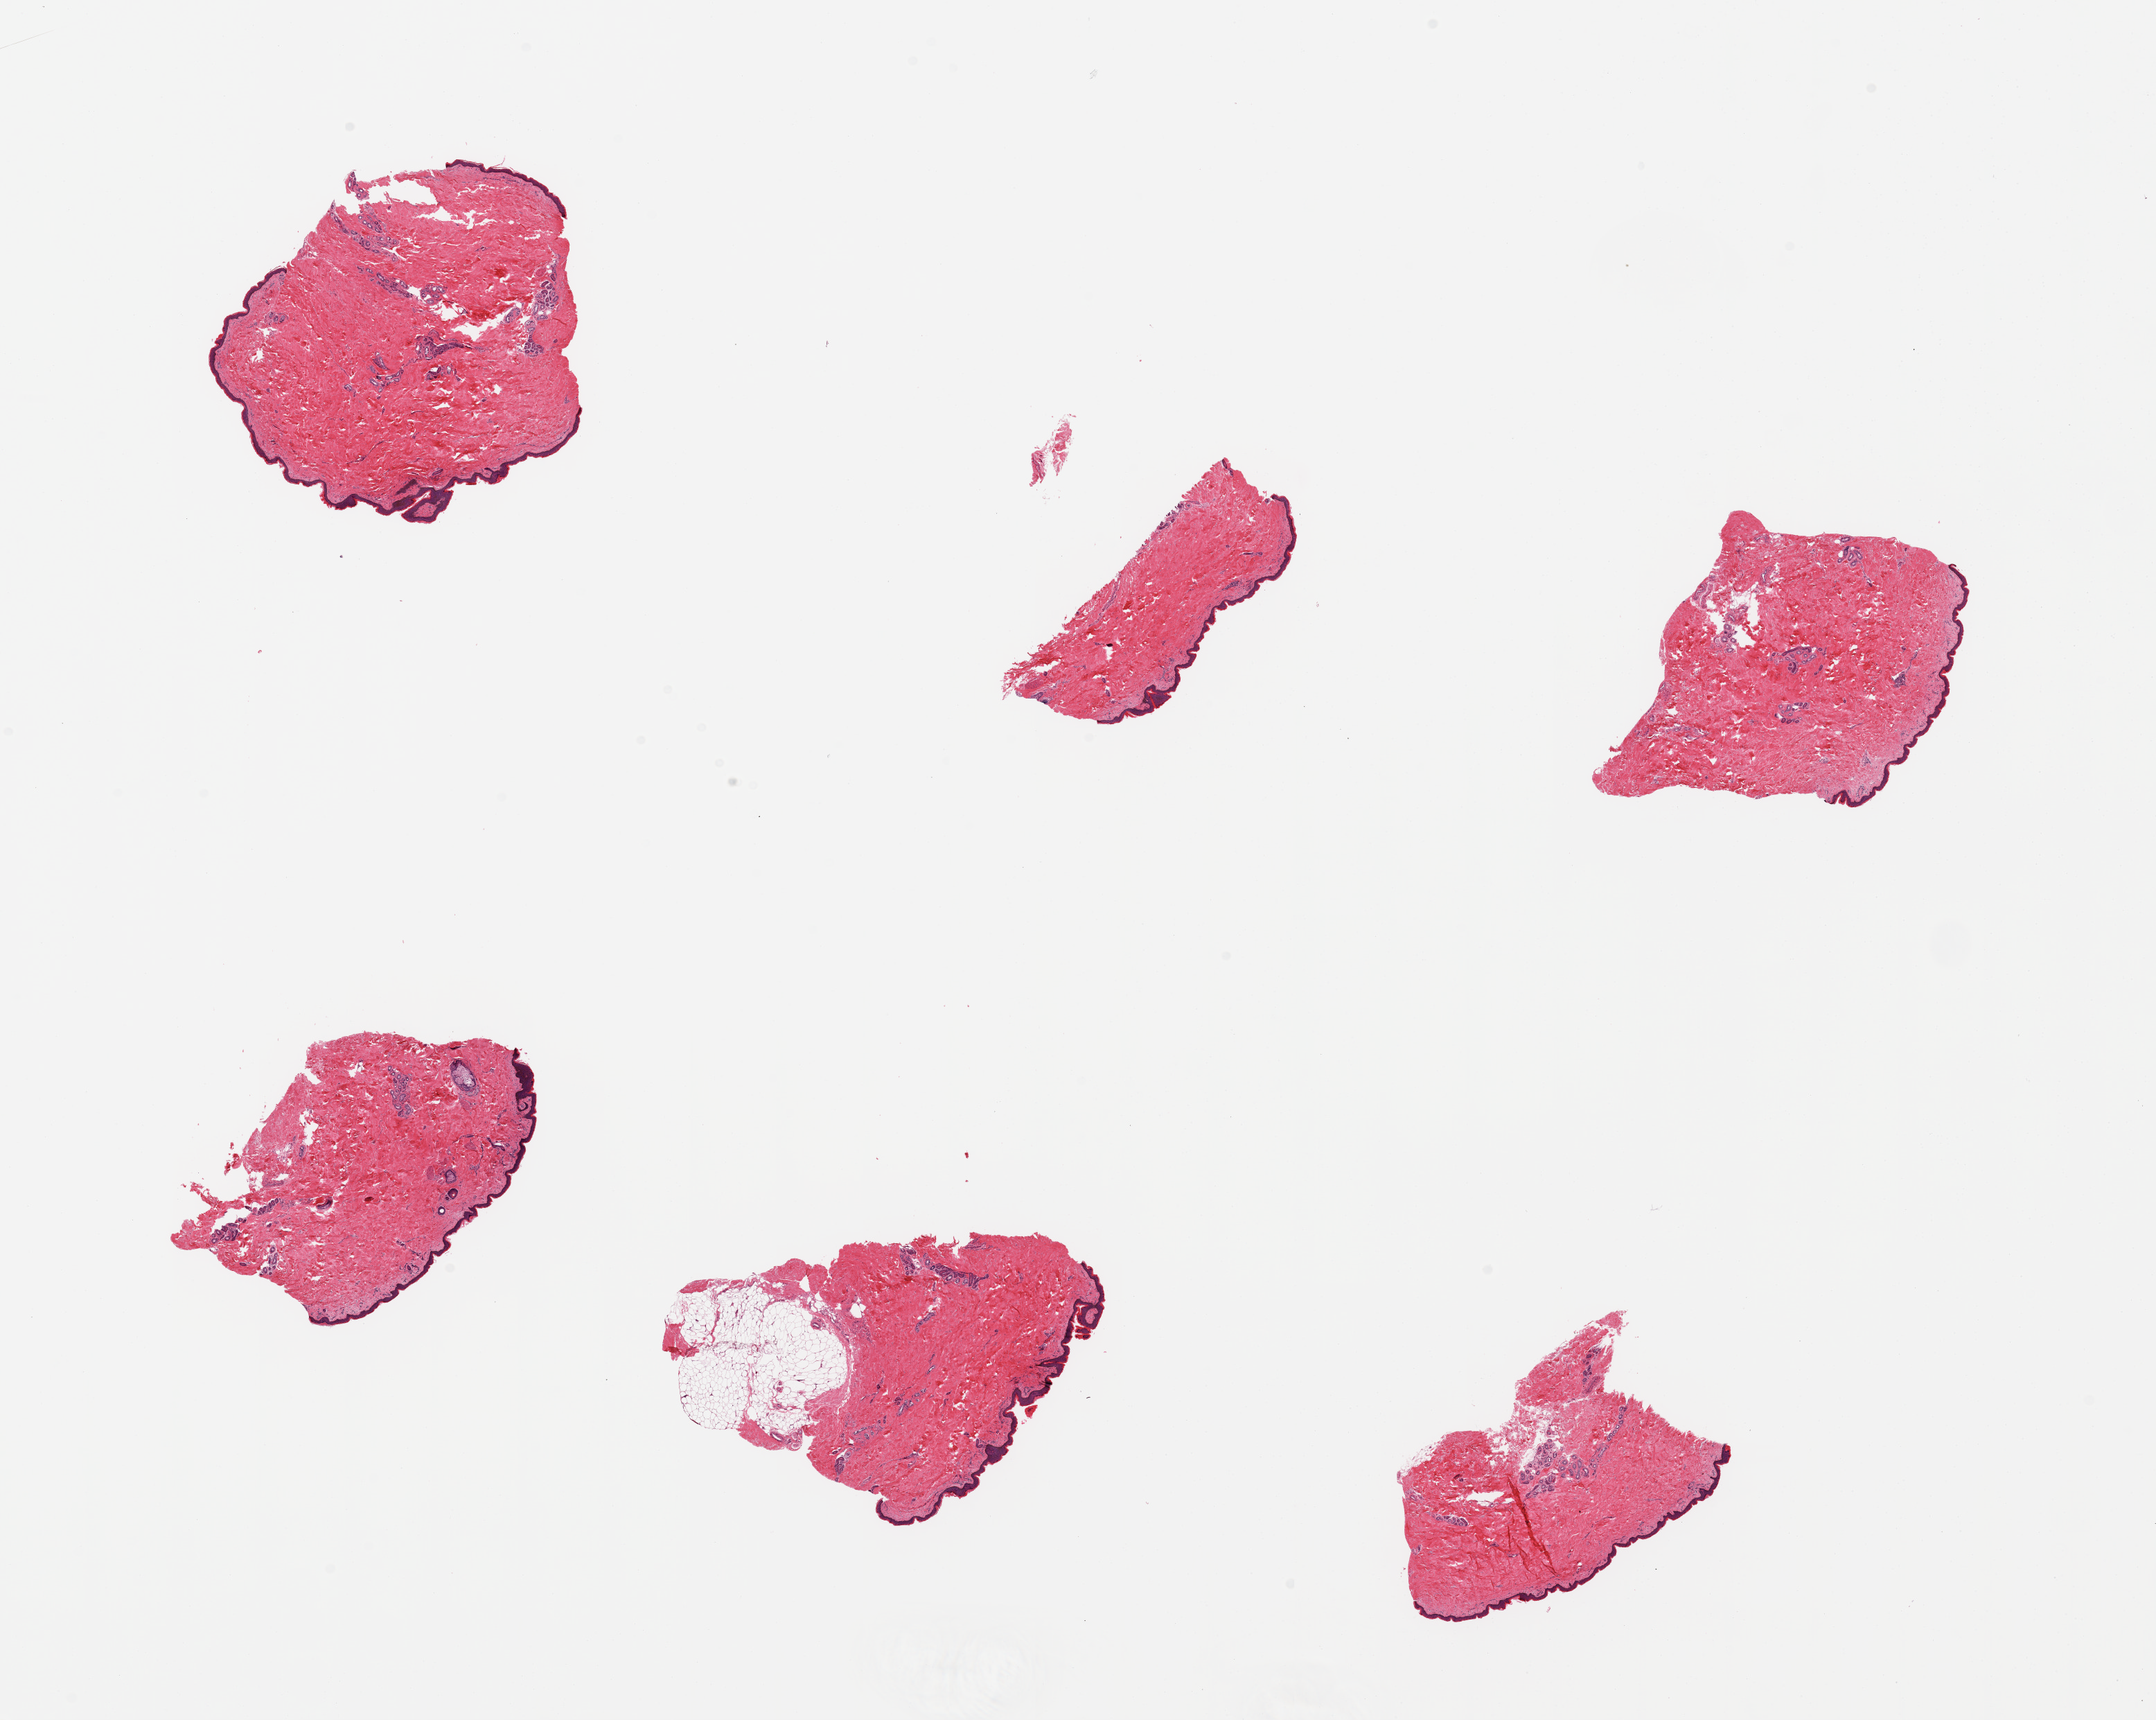
Whole-slide image, hematoxylin and eosin (H&E) stain, brightfield, low-resolution overview of the scanned area, about 24.6 x 19.6 mm; PAXgene-fixed paraffin-embedded (PFPE) section; sampled site (target tissue): skin of lower leg; donor tissue sample. Donor sex: male.
Reviewer comment on this tissue sample: 6 pieces, focal adherent fat up to ~1.5 mm; sqaumous epithelium is ~50-60 microns.